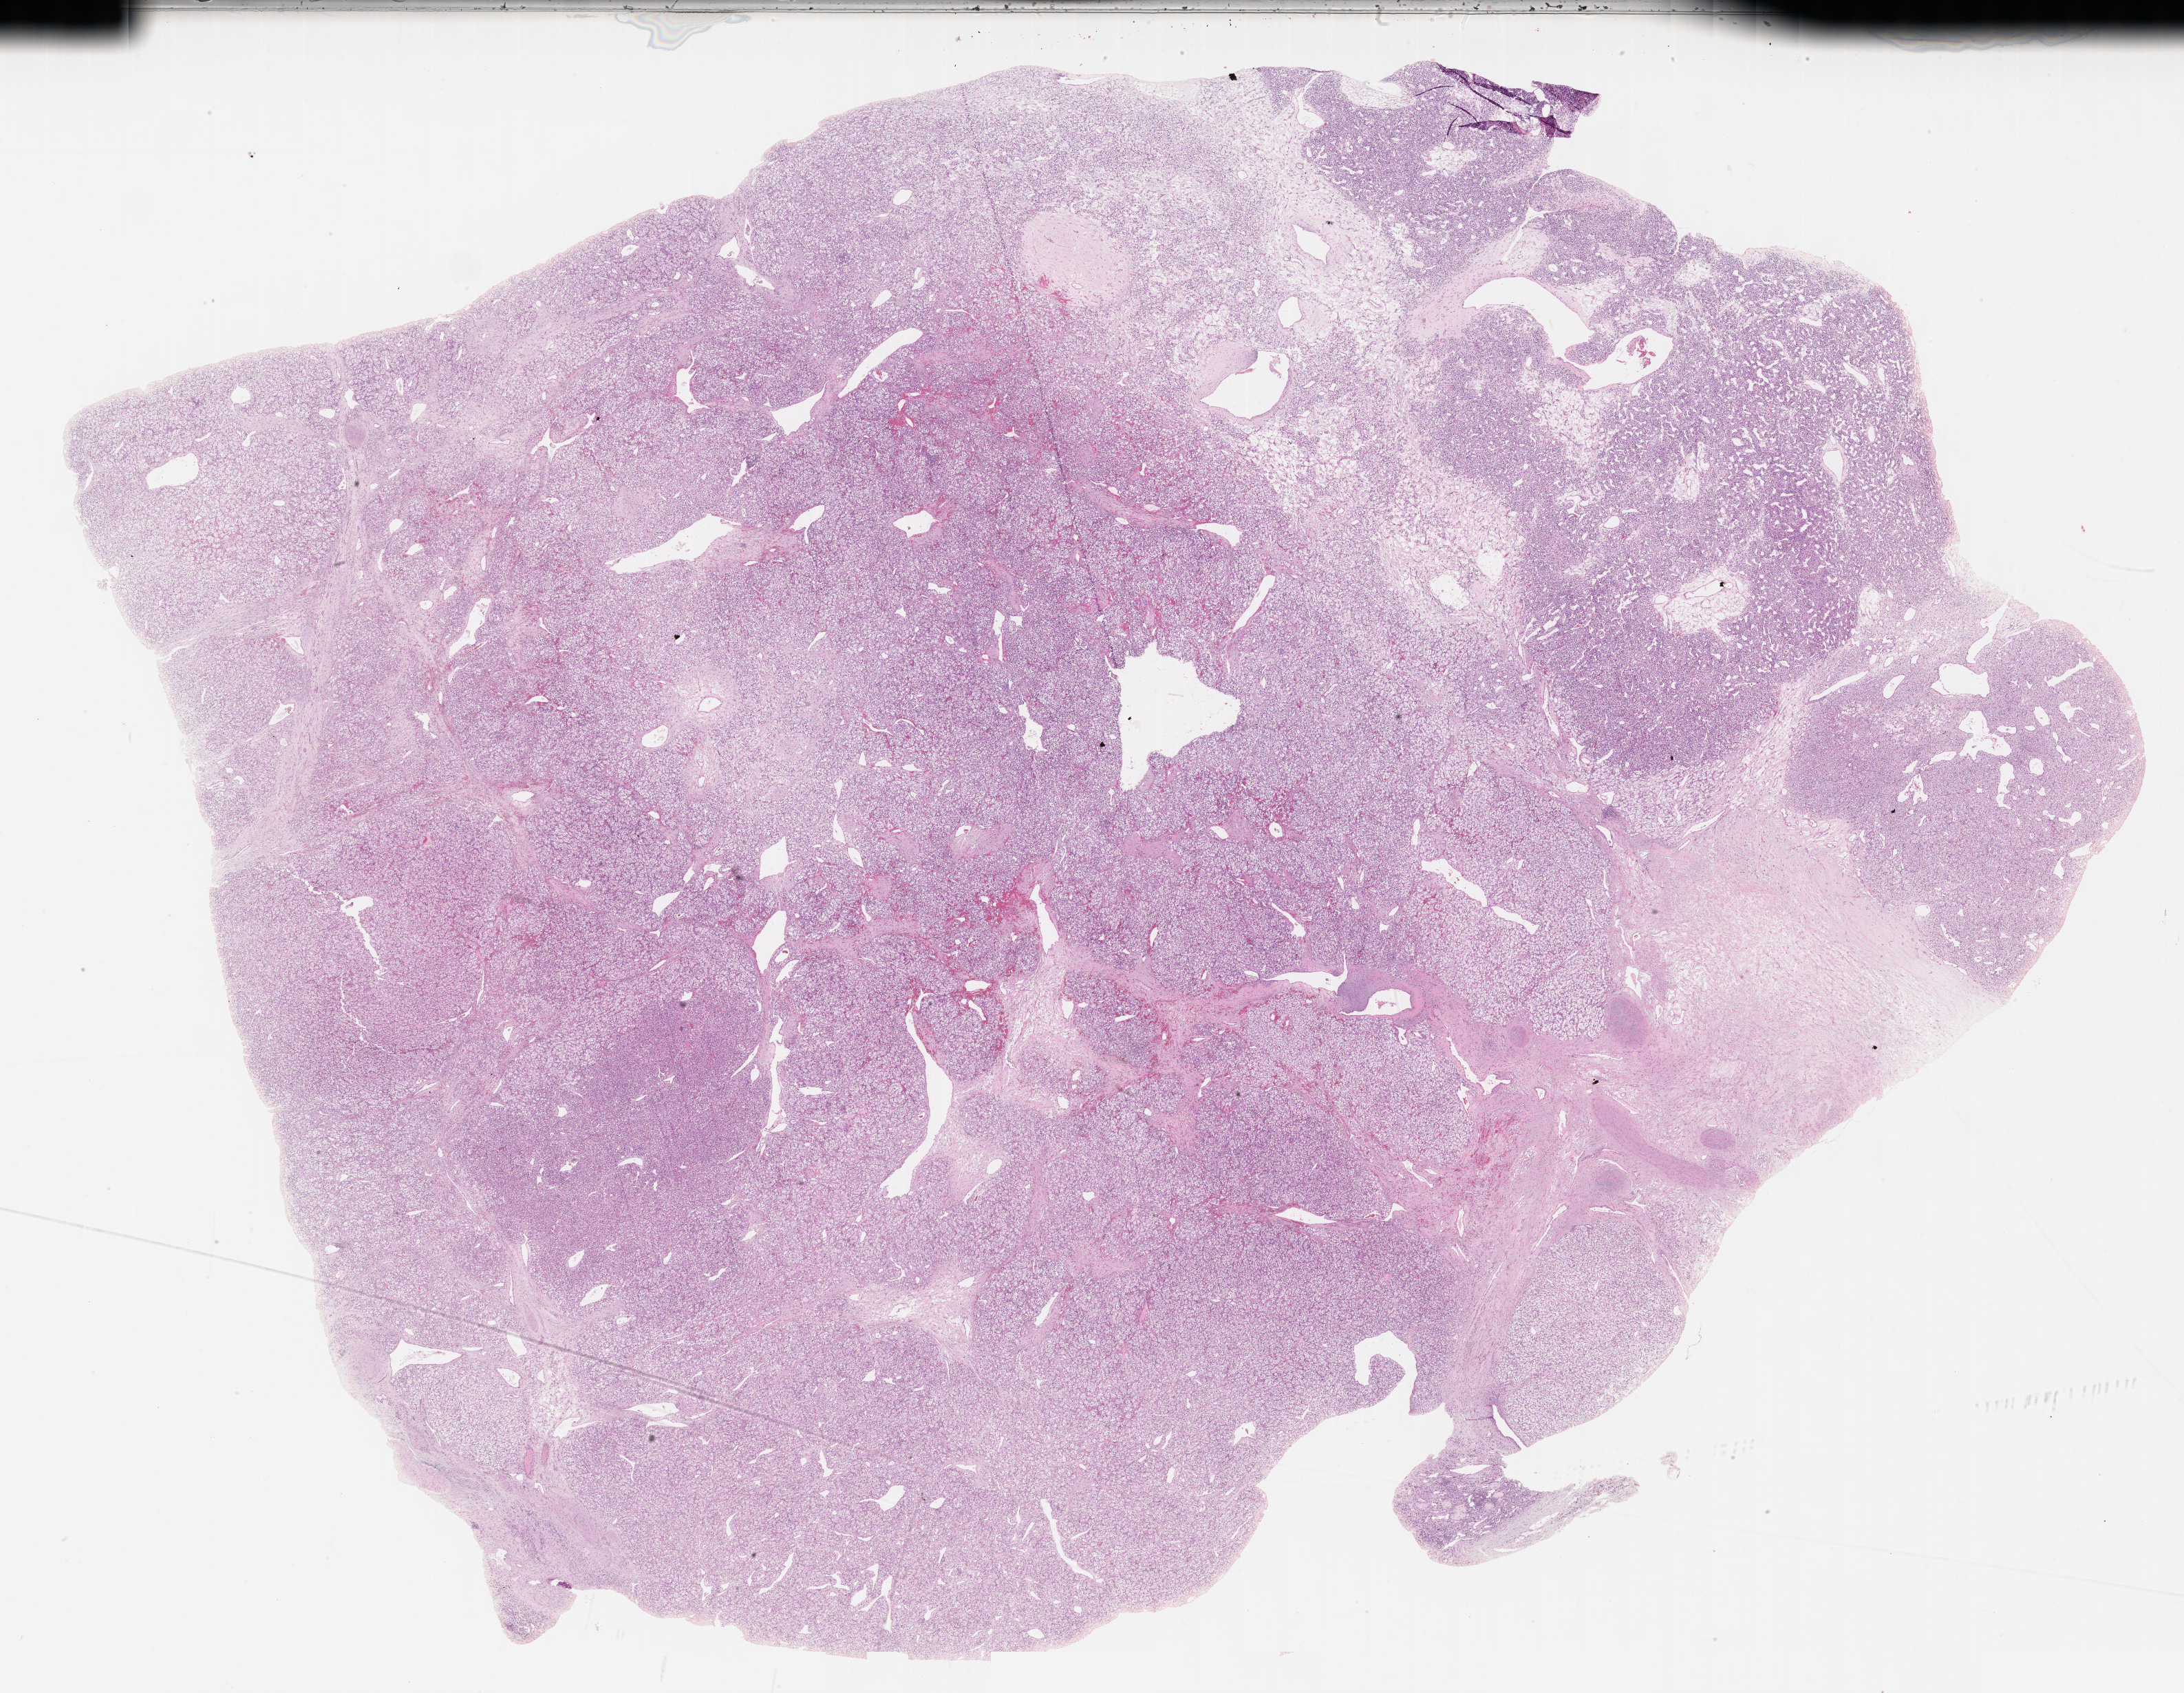
Whole-slide histology image, Hematoxylin and eosin (H&E) stained — a low-resolution overview of the entire scanned area, about 25.7 x 19.9 mm (slide scanned at 40x). Formalin-fixed paraffin-embedded (FFPE) diagnostic section. Primary tumour sample from the kidney. Female, age 60 years at initial diagnosis. Histologic grade: G3 (poorly differentiated).
AJCC pathologic stage: IV (7th edition). Histologic diagnosis: Clear cell adenocarcinoma, NOS. Lymph nodes positive (case pathology): 0 of 13 examined.